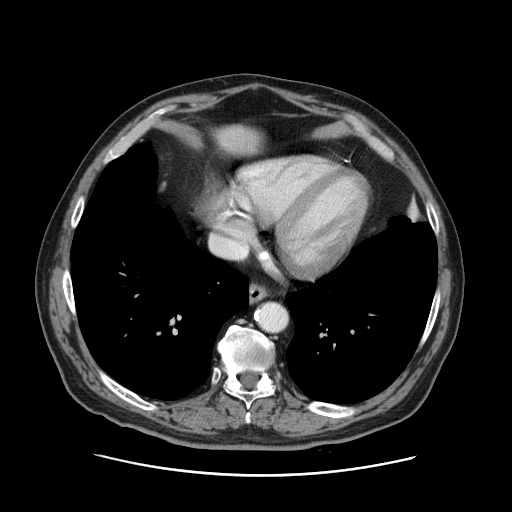
Contrast-enhanced abdominal CT, one axial slice. Slice 125 of 141 in the series (ordered by position). 120 kVp. Intravenous contrast given. Soft-tissue window (W 400 / L 40 HU). 512 × 512 image matrix, field of view 395 × 395 mm. Male patient, age 72 years. From the clinical record (not read from this slice): diagnosis: colorectal cancer liver metastases, imaged before liver resection; multiple liver metastases: yes; largest metastasis: 5.4 cm; chemotherapy before resection: yes.
Outlined on this slice (manually delineated by an expert):
- liver: bounding box <215,125,260,154> (left, top, right, bottom; pixels)
- planned liver remnant (the part of the liver to remain after resection): <215,125,261,154>